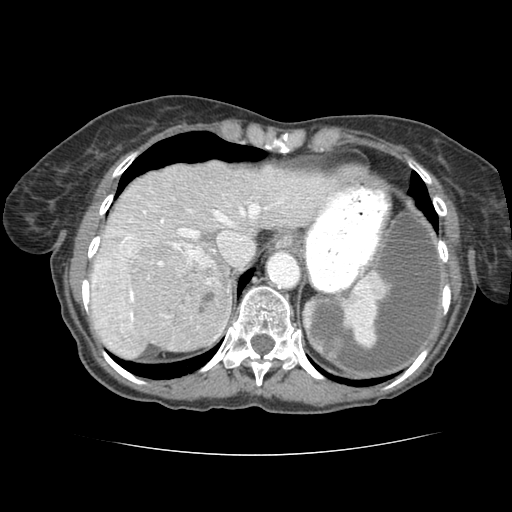
Contrast-enhanced abdominal CT (liver protocol), one axial slice. Position 64 of 77 along the scan axis. Reconstruction kernel STANDARD. 120 kVp. Soft-tissue window (W 400 / L 40 HU). 2.5 mm slice thickness. 512 × 512 image matrix, field of view 340 × 340 mm. From the clinical record (not read from this slice): diagnosis: hepatocellular carcinoma (patient treated with transarterial chemoembolisation; whether this scan precedes or follows treatment is not stated here); TNM stage (as recorded): Stage-I; Child-Pugh class: A; tumour differentiation: well differentiated; tumour size: 7.6 cm.
Annotated regions visible in this slice (semi-automatic segmentation, software-assisted and operator-edited):
- liver parenchyma outside the tumour (the mass and vessels are separate outlines, so this box may not span the whole liver): box from (x=88, y=162) to (x=325, y=350) px
- mass: (x=129, y=243)–(x=226, y=344)
- liver vessels: (x=122, y=216)–(x=228, y=324)